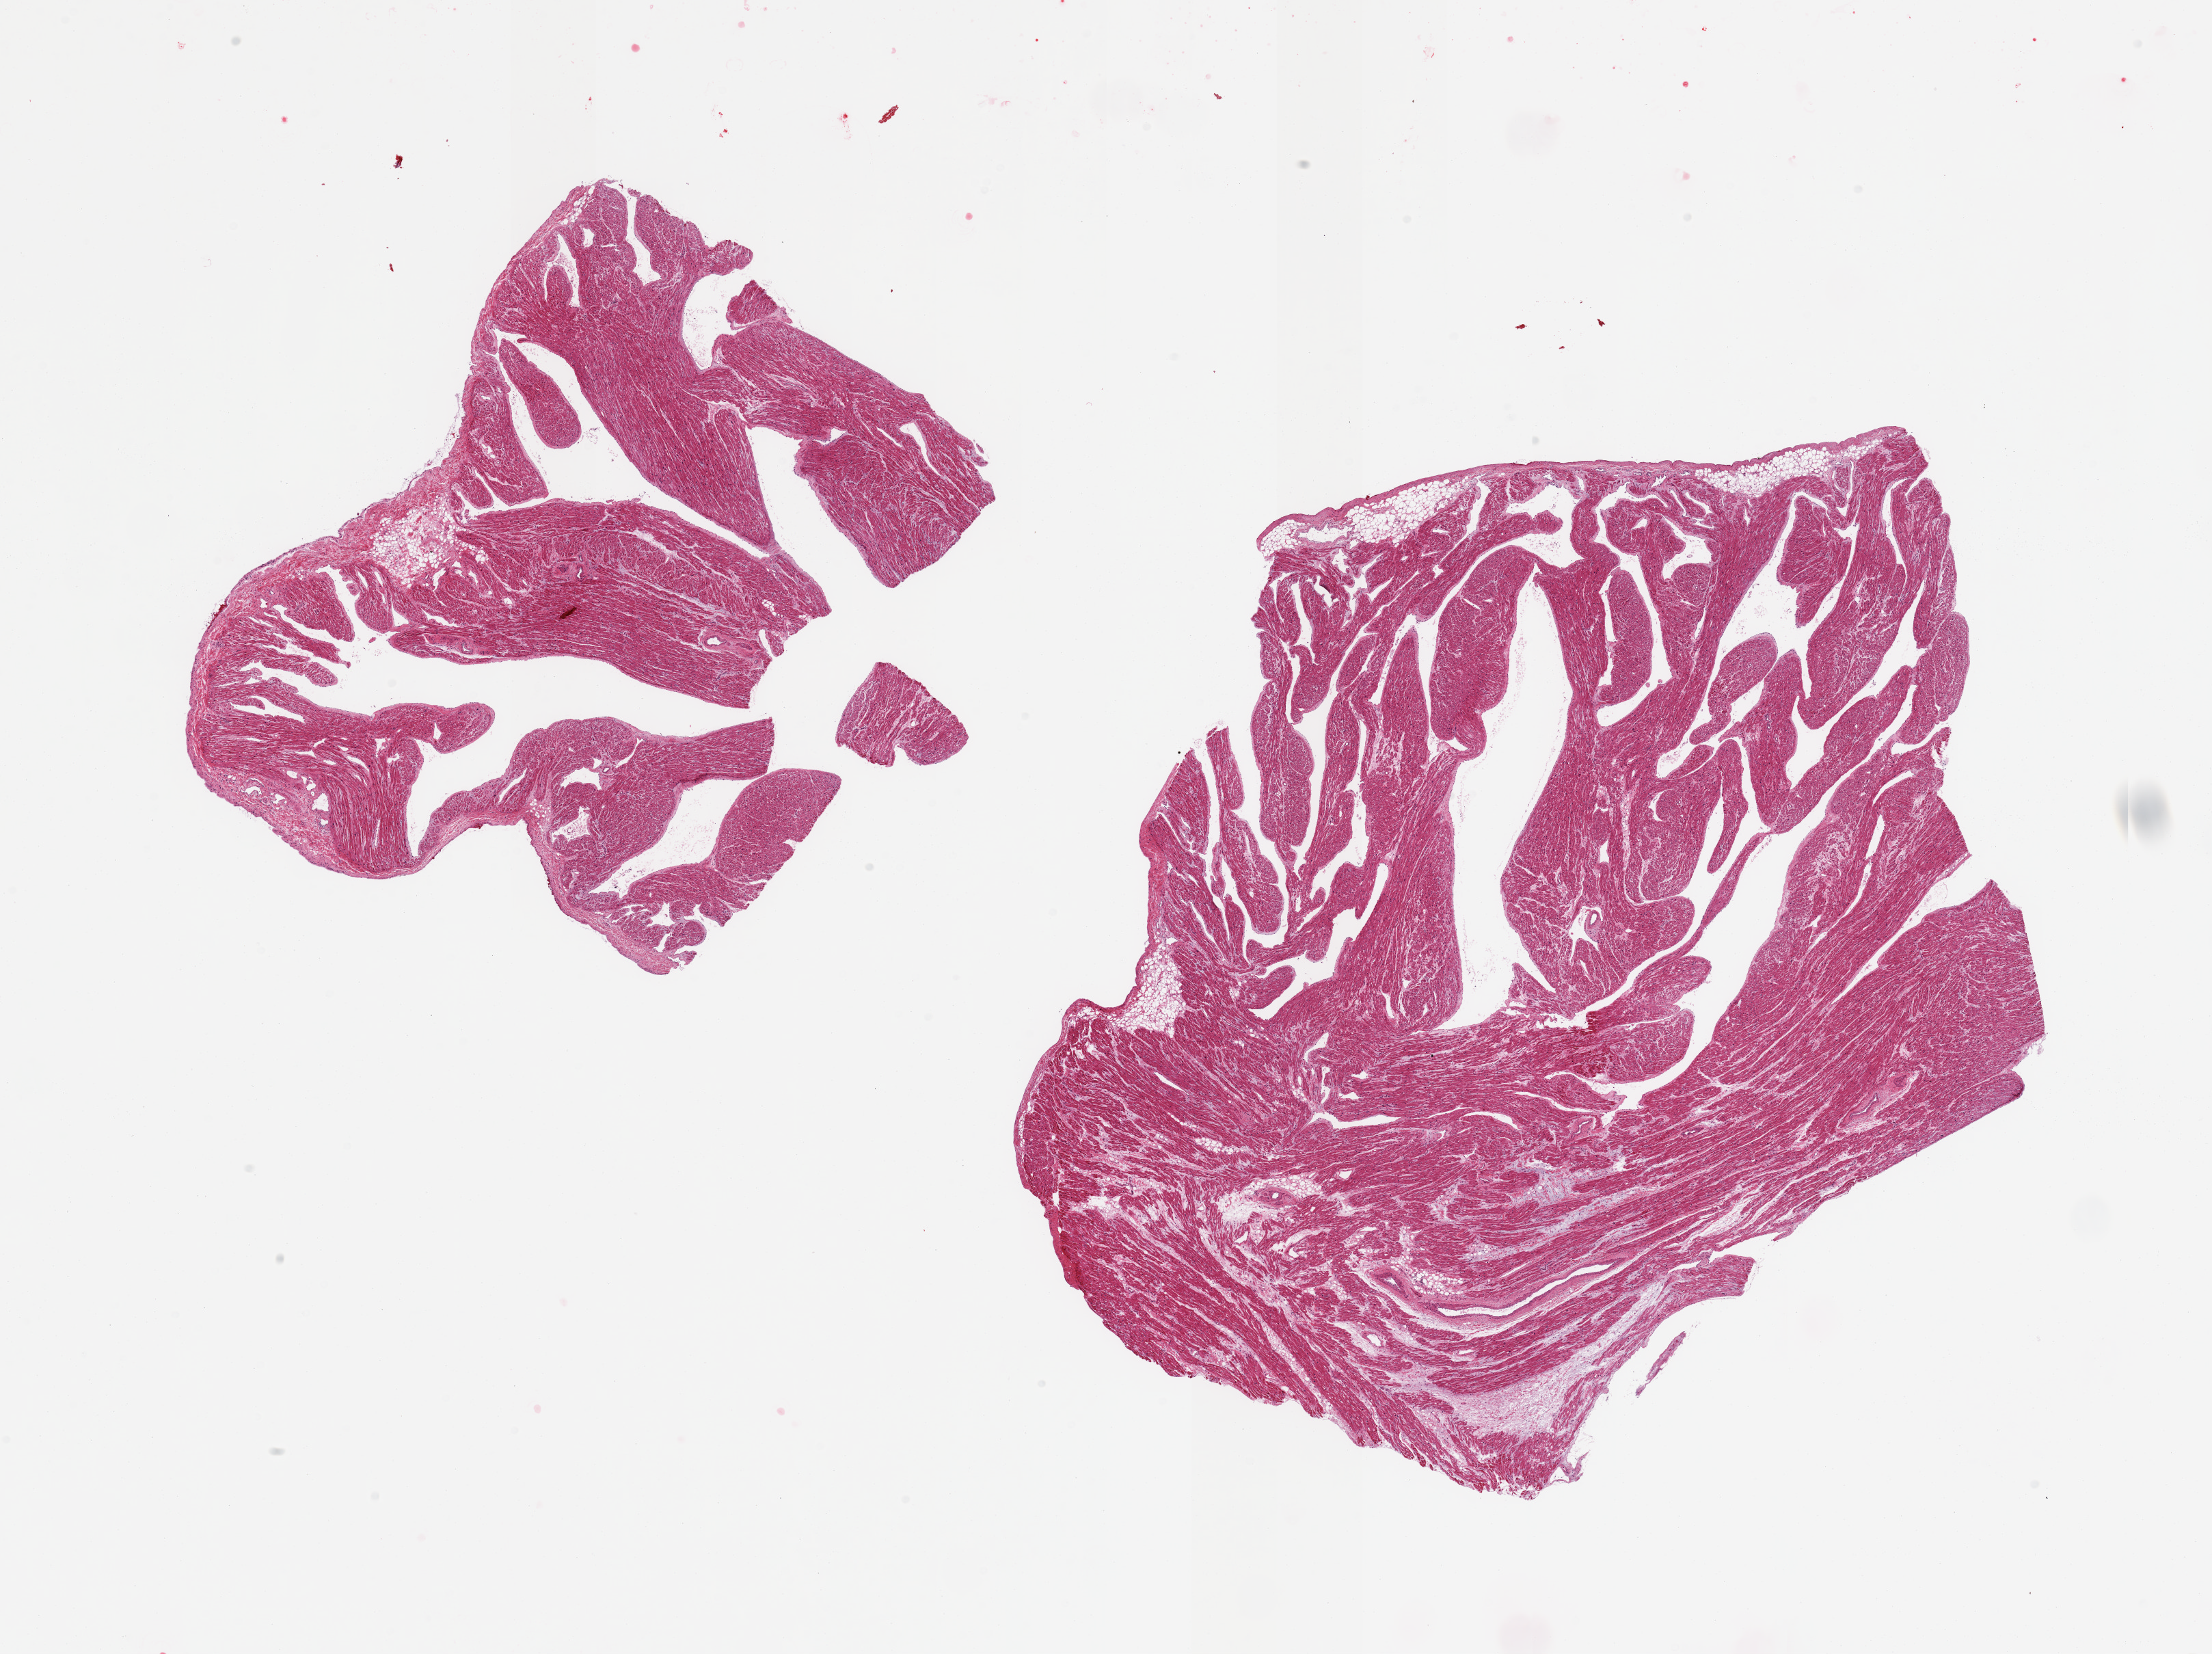
Haematoxylin and eosin whole-slide image — shown as a low-resolution overview of the whole scanned area (about 25.6 x 19.1 mm, from a 20x scan). PAXgene-fixed, paraffin-embedded tissue. Target tissue: auricular appendage. Tissue donor sample. Donor: male.
* pathologist's review note for this sample: 2 pieces; 5-10% internal (interstitial, perivascular and subepicardial) fat